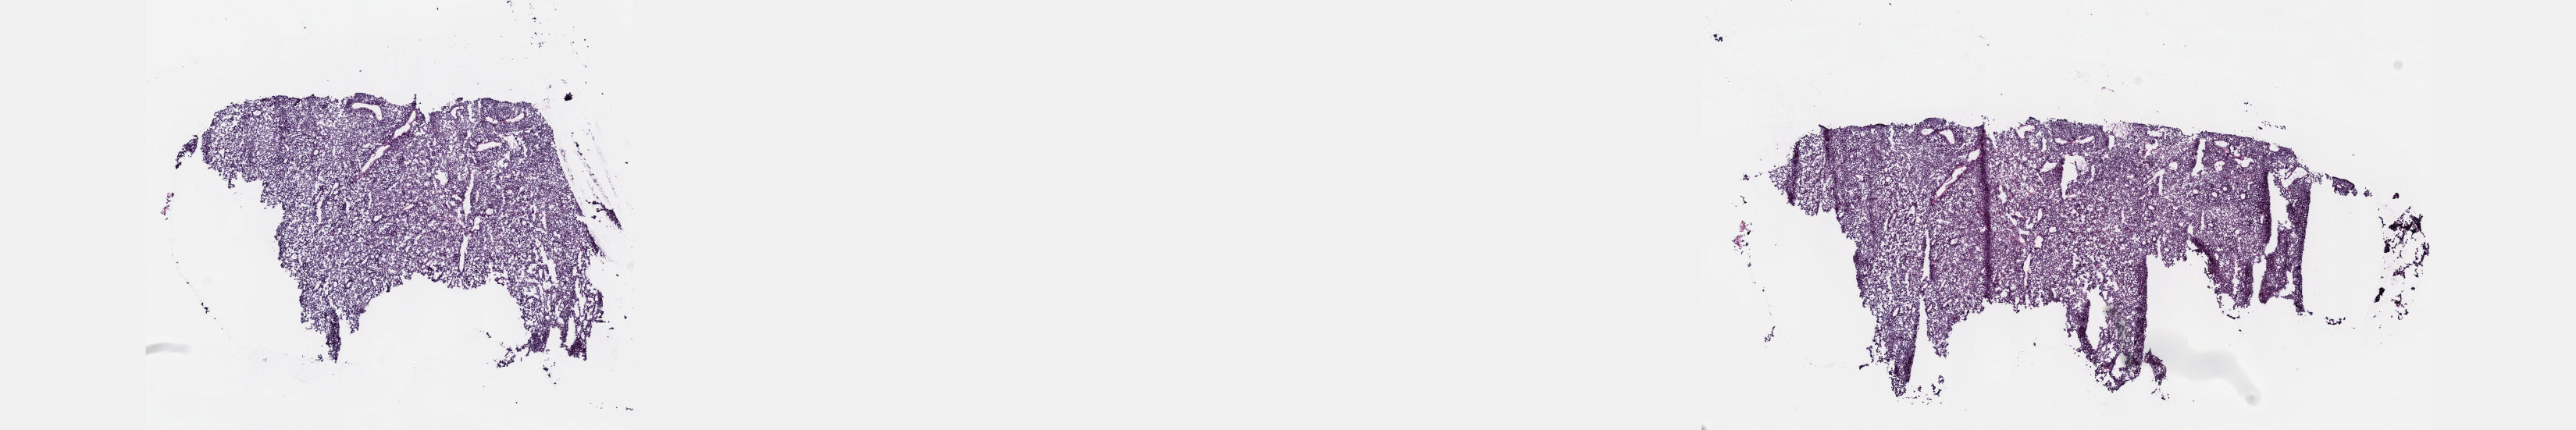
H&E-stained whole-slide image, whole scanned area (about 26.7 x 4.5 mm, from a 40x scan) shown as a low-resolution overview, frozen section from the top of the tissue portion, metastatic tumour sample, sampled site: colon. Male patient. Pathologist review of this section (percent, as recorded): tumour cells 100%, tumour nuclei 95%, normal cells 0%, stromal cells 0%, necrosis 0%. Infiltration values recorded for this section: lymphocyte infiltration 0%, monocyte infiltration 0%, neutrophil infiltration 0%.
This section: metastatic tumour tissue. Patient diagnosis: Epithelioid cell melanoma.